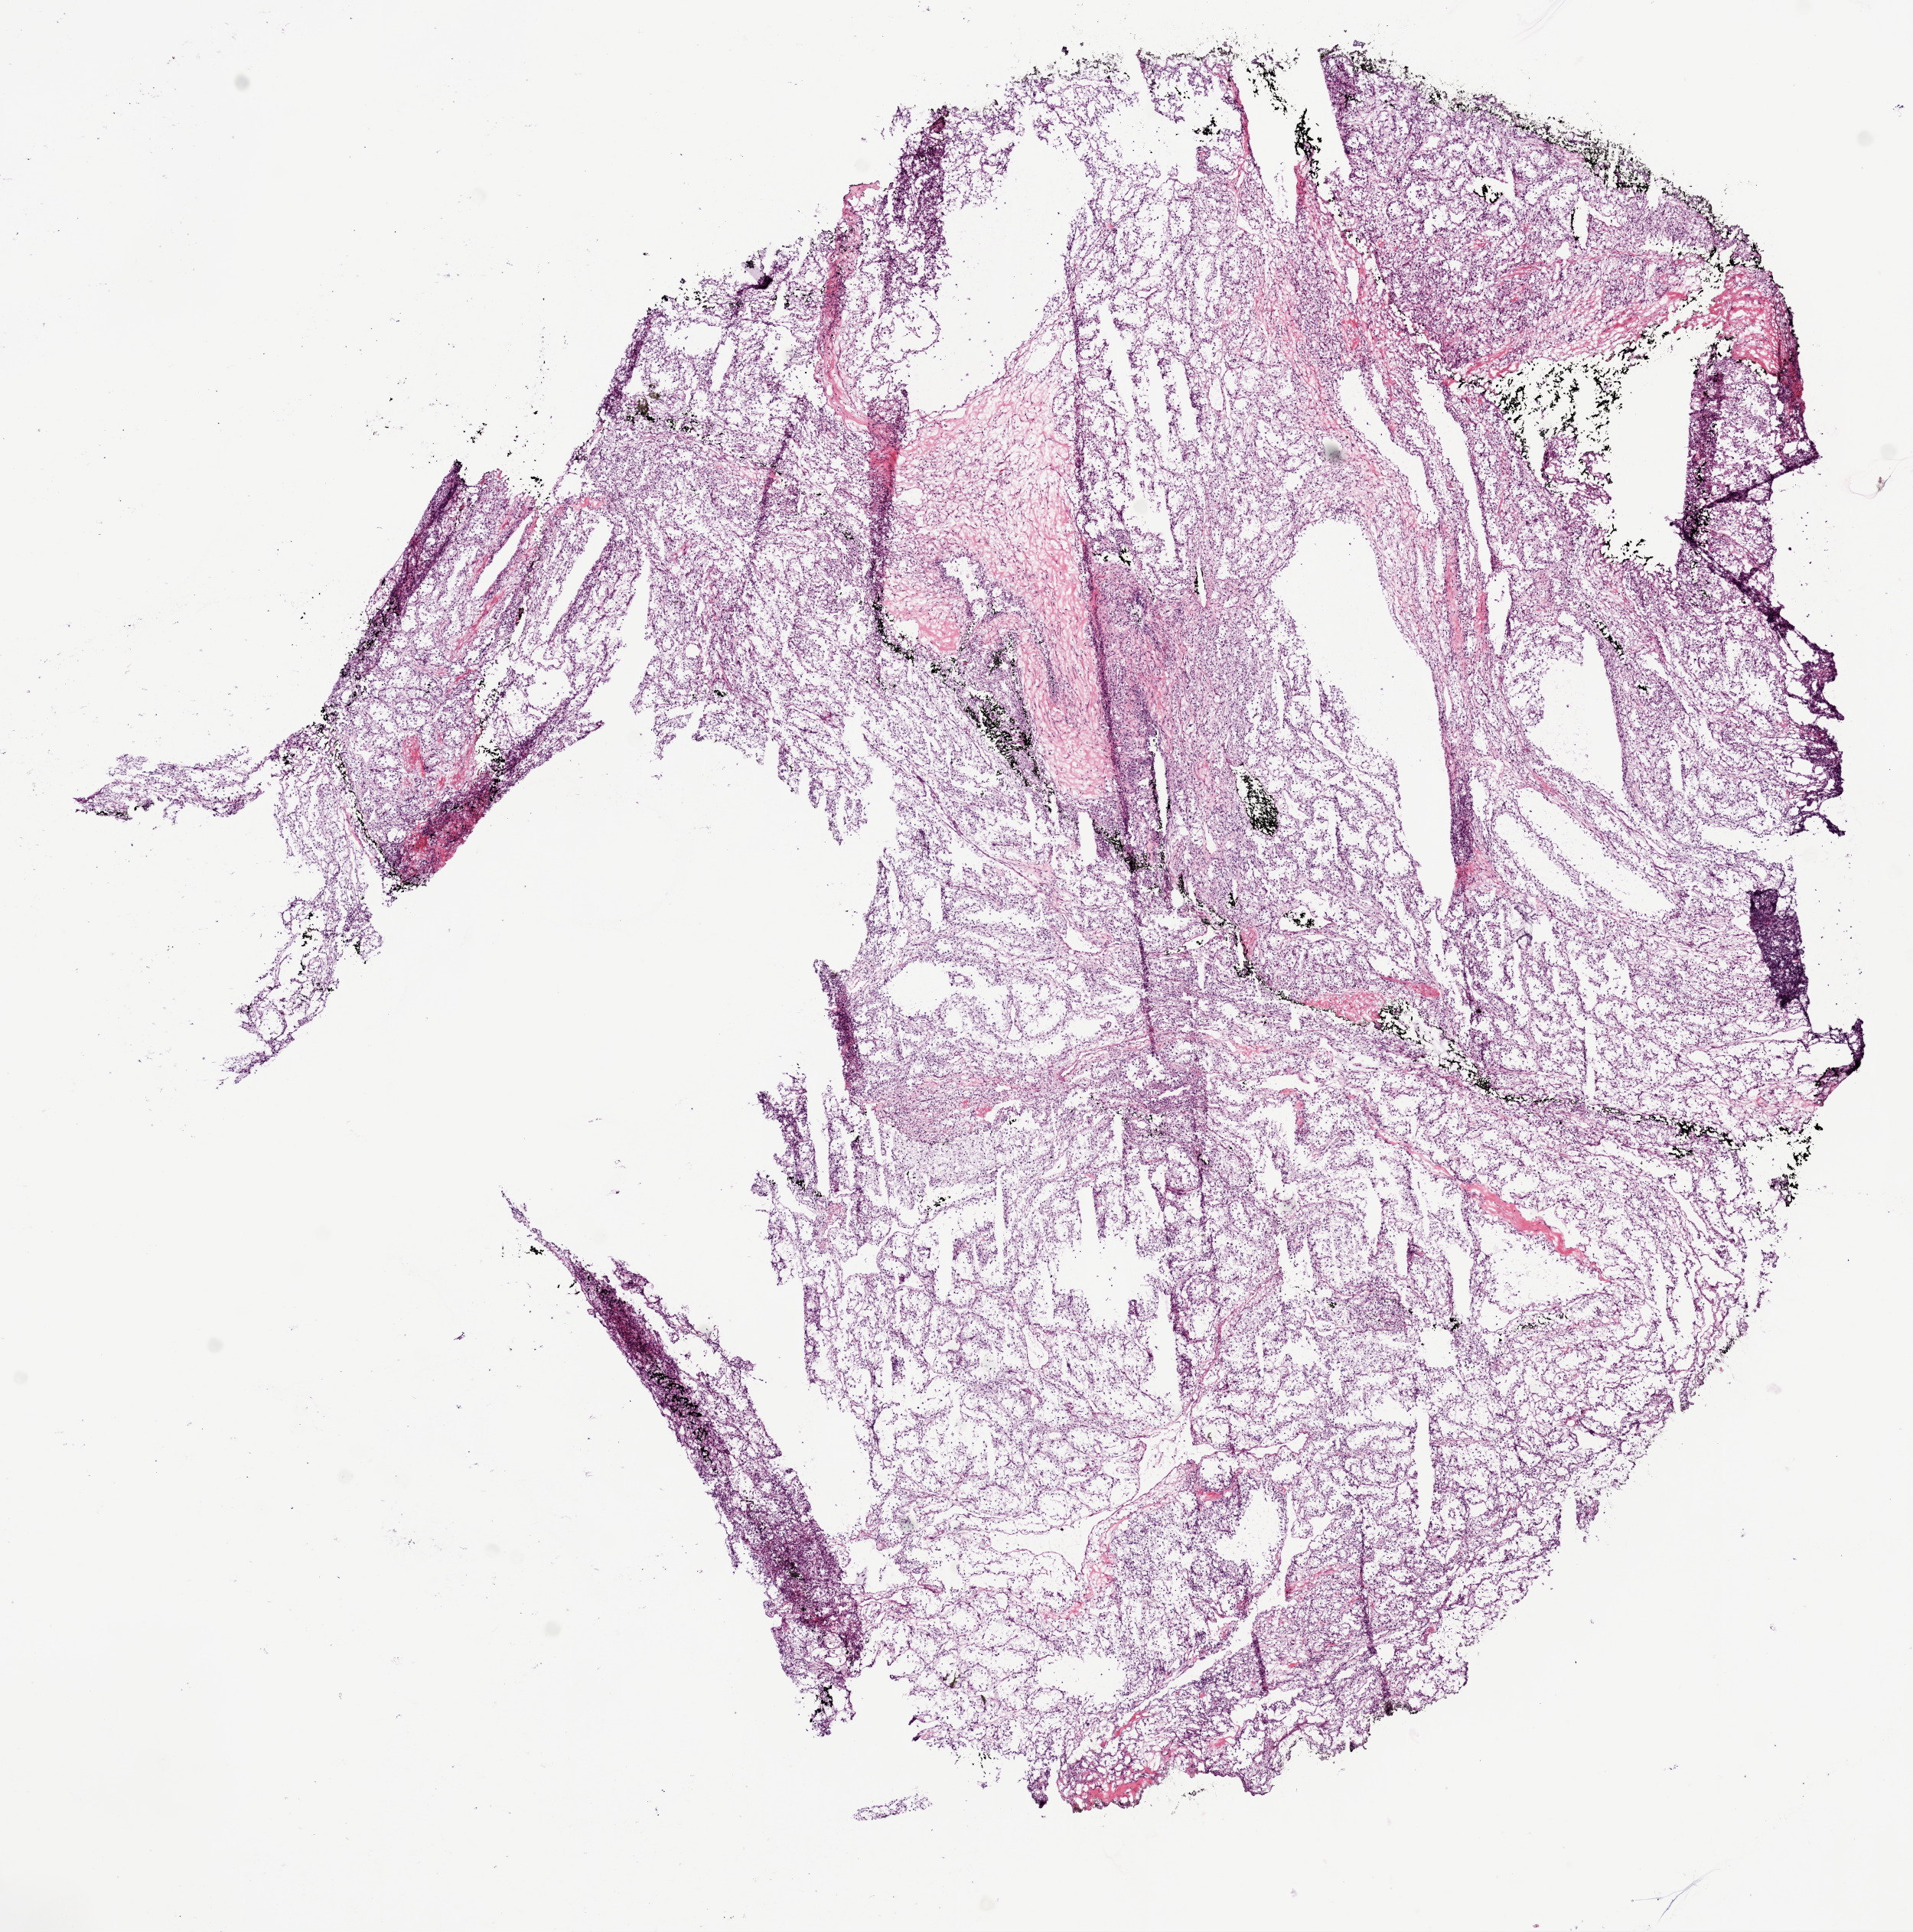
Whole-slide histology image, Hematoxylin and eosin (H&E) stained — whole scanned area (about 10.0 x 10.1 mm) shown as a low-resolution overview, frozen section from the bottom of the tissue portion, primary tumour sample from the kidney. Female, age 77 years at initial diagnosis. Histologic grade: G2 (moderately differentiated). Composition of this section per pathologist review: tumour cells 90%, tumour nuclei 80%, normal cells 0%, stromal cells 10%, necrosis 0%.
Laterality: right. Histologic diagnosis: Clear cell adenocarcinoma, NOS. AJCC pathologic stage: III.